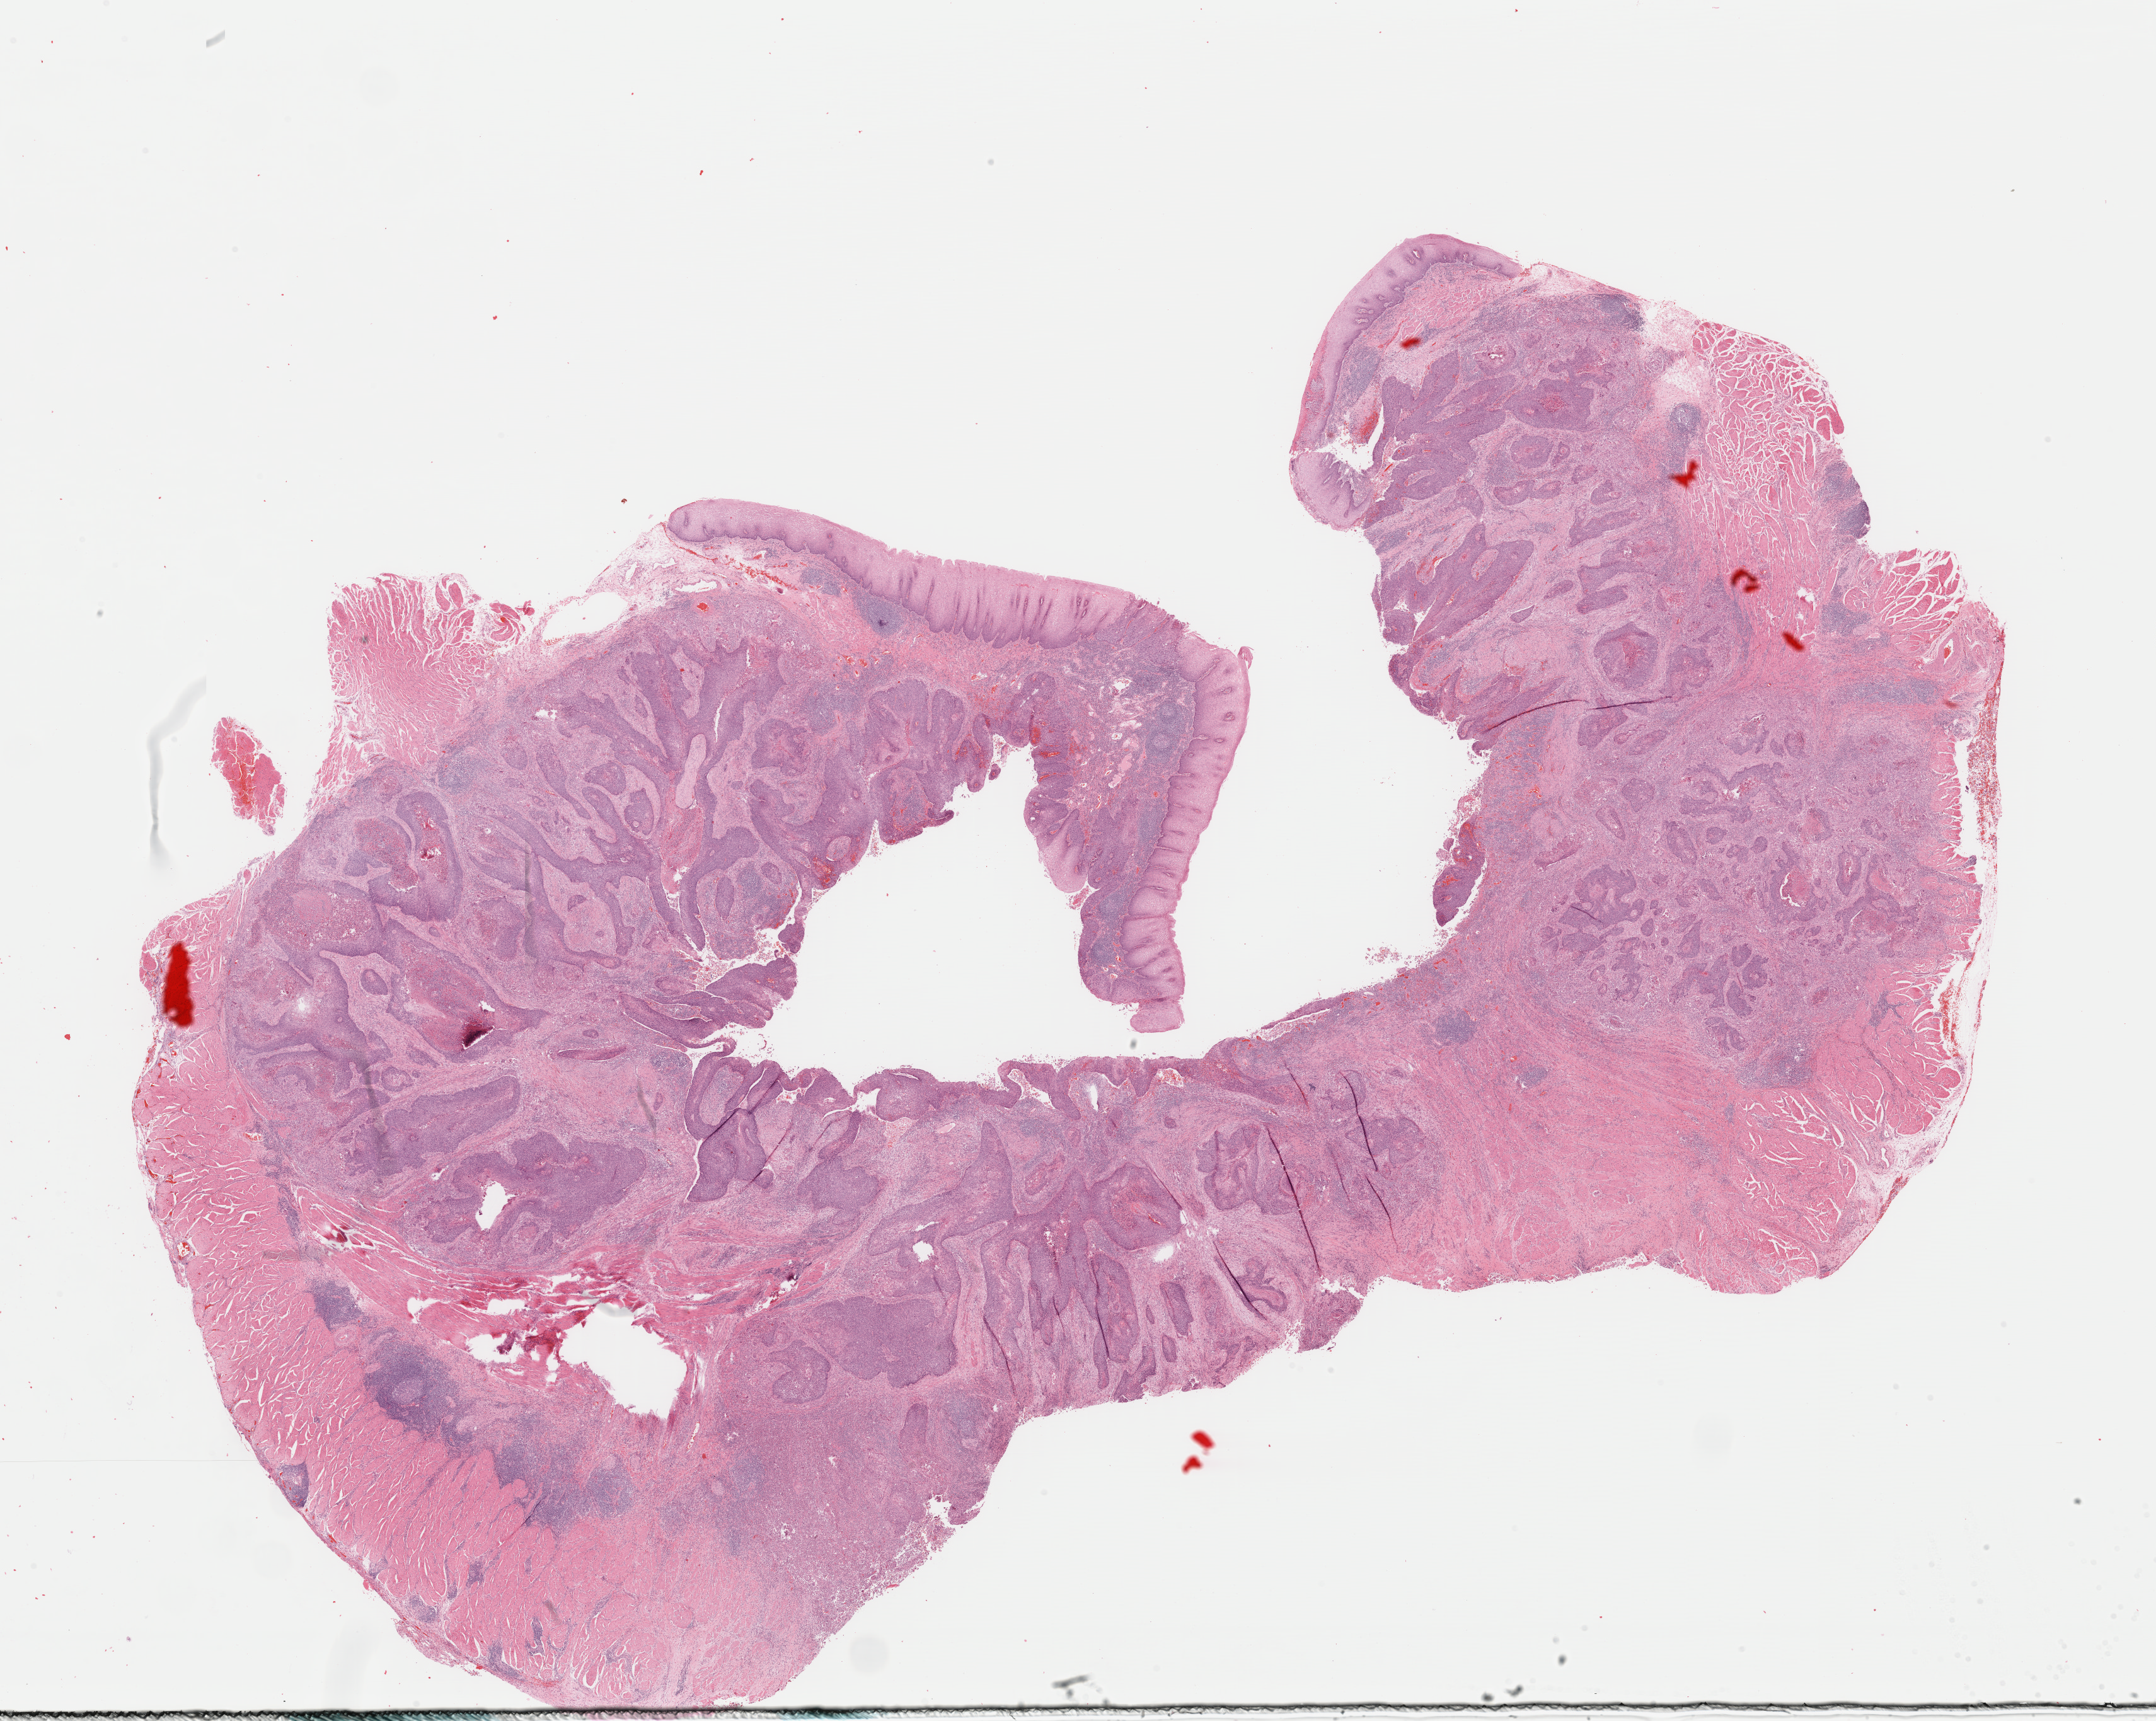
Whole-slide histology image, H&E — whole scanned area (about 27.0 x 21.5 mm, slide scanned at 40x) shown as a low-resolution overview, FFPE section, esophagus, primary tumour sample. Male, age 53 years at initial diagnosis. Histologic grade: G2 (moderately differentiated).
AJCC pathologic stage: IIIA (7th edition). Histologic diagnosis: Squamous cell carcinoma, NOS (lower third of esophagus). TNM: T4 N0 M0.